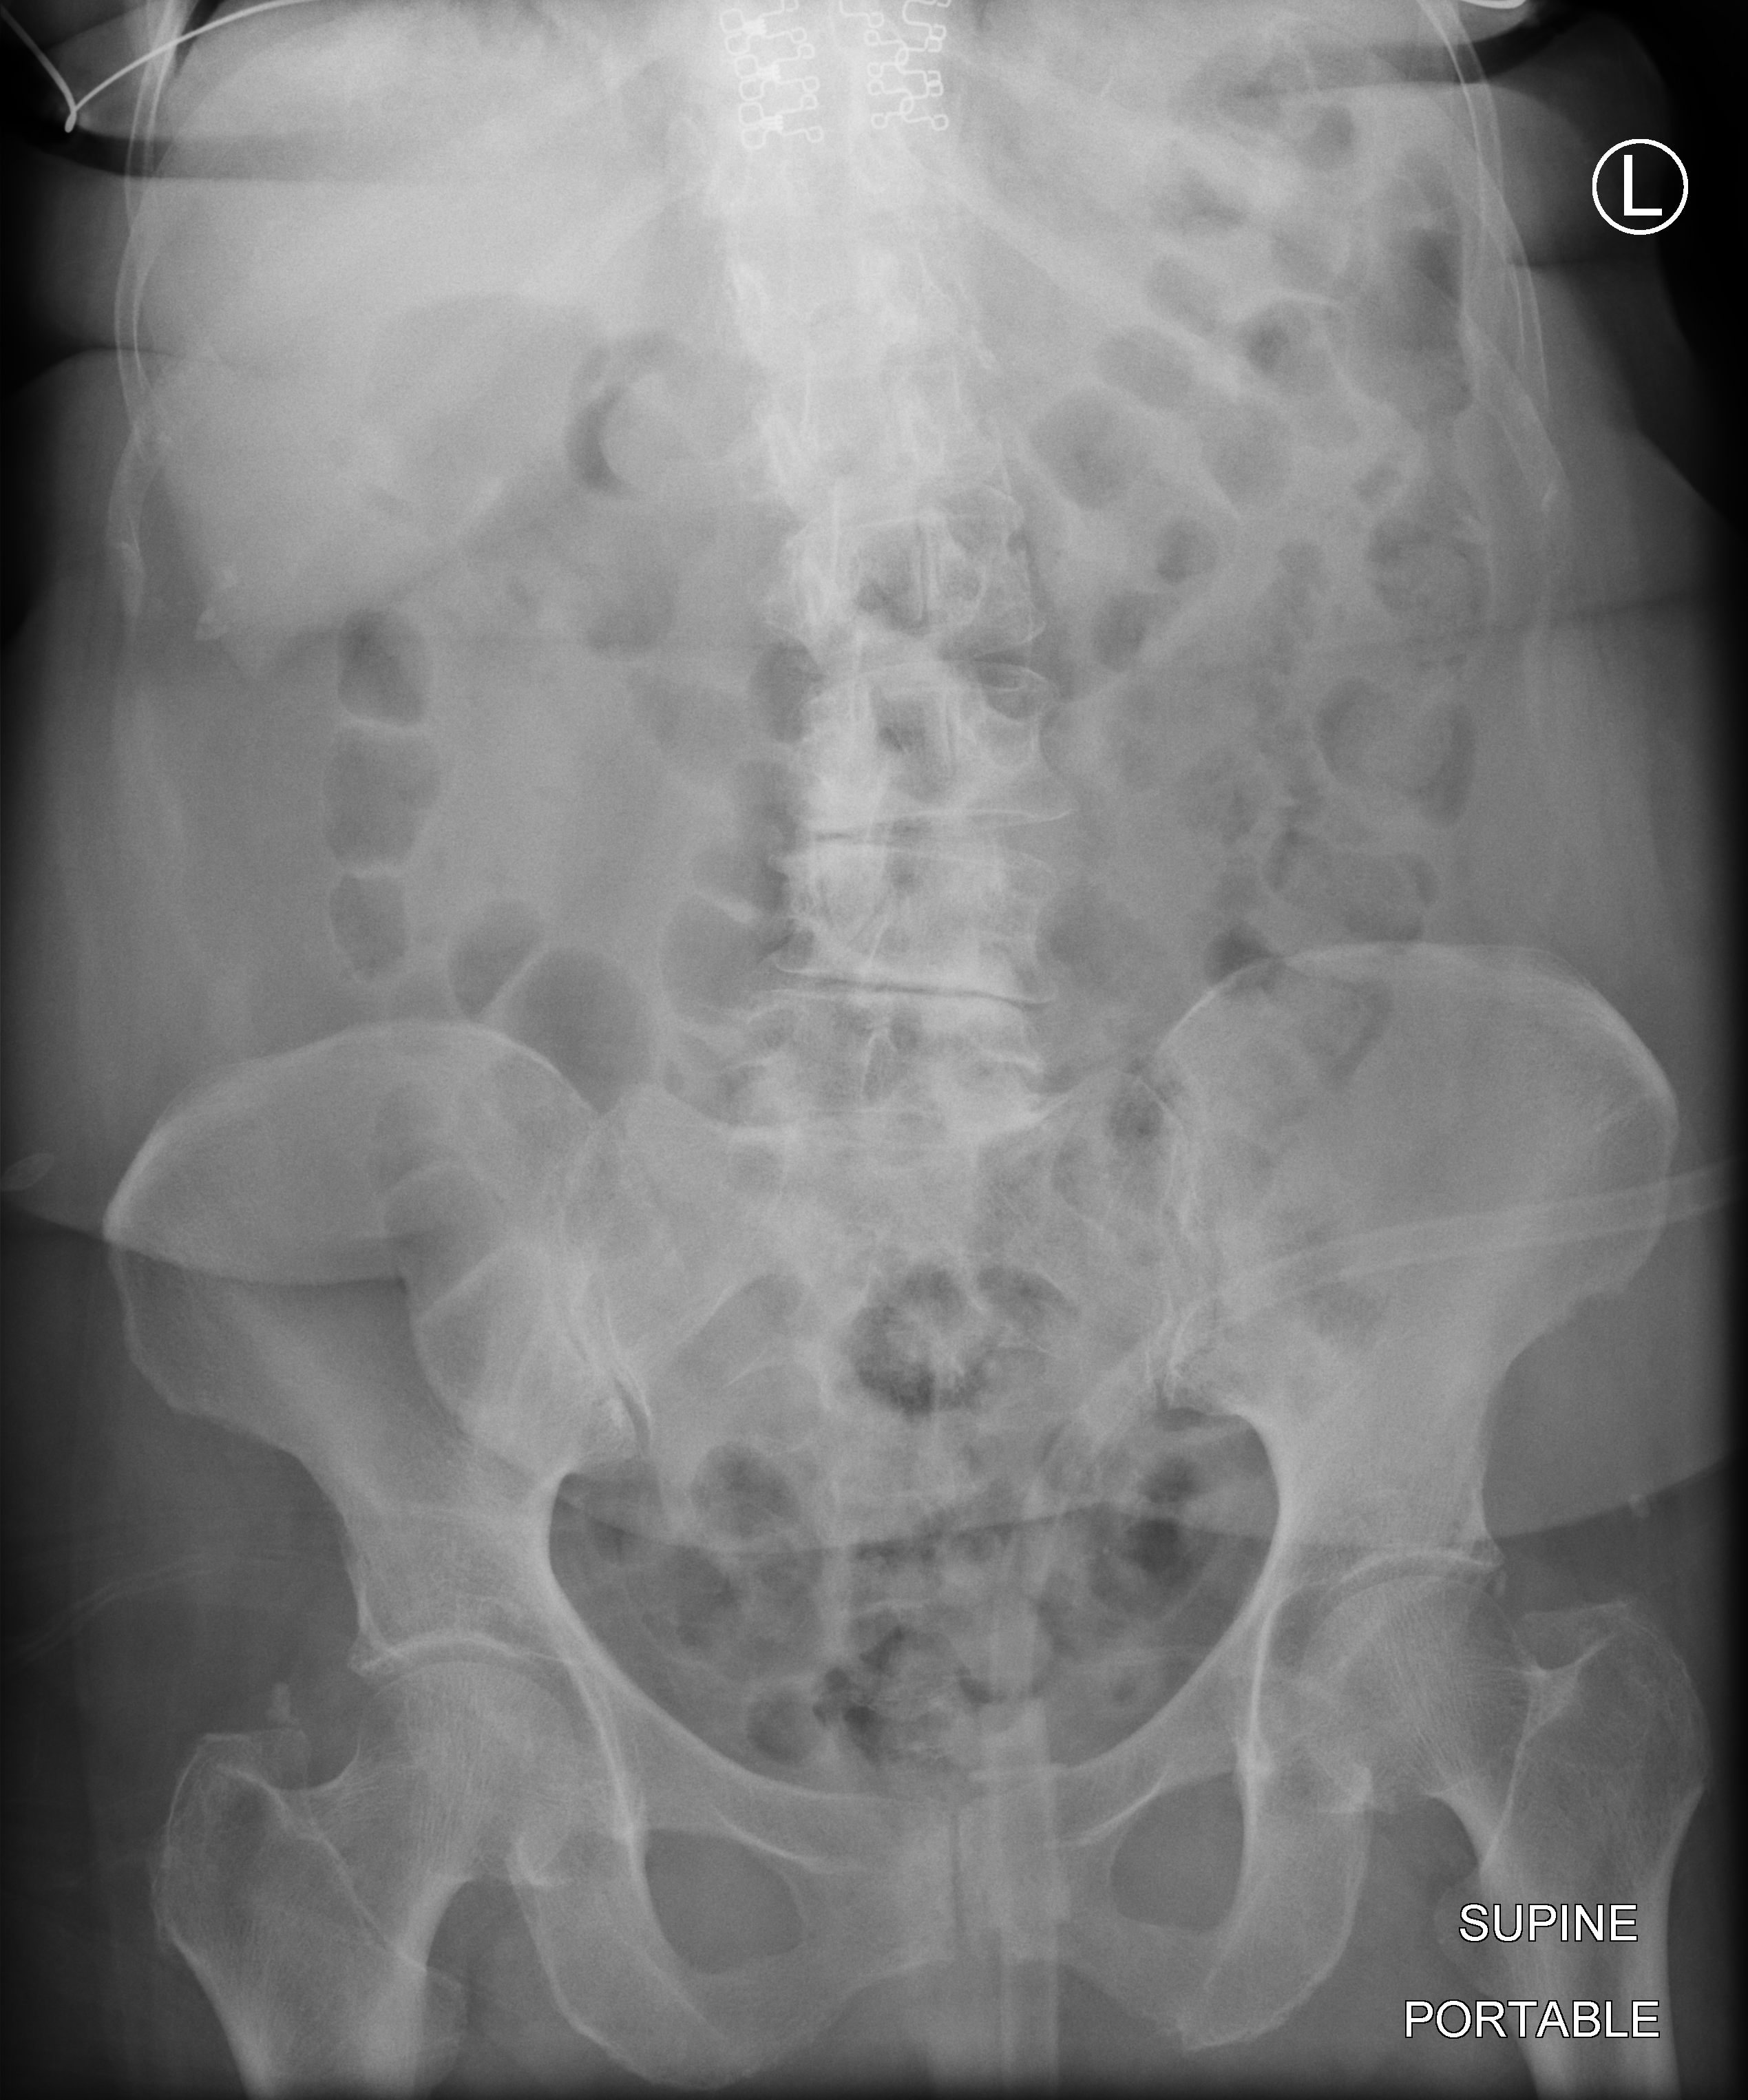
Bedside abdomen radiograph (computed radiography), anteroposterior (AP) projection. Patient hospitalised with COVID-19; female, aged 75–90 years.
Admission-level facts for this patient (not findings on this image; timing relative to this image not recorded): COPD (admission record): no; mechanically ventilated during this hospital stay: no.